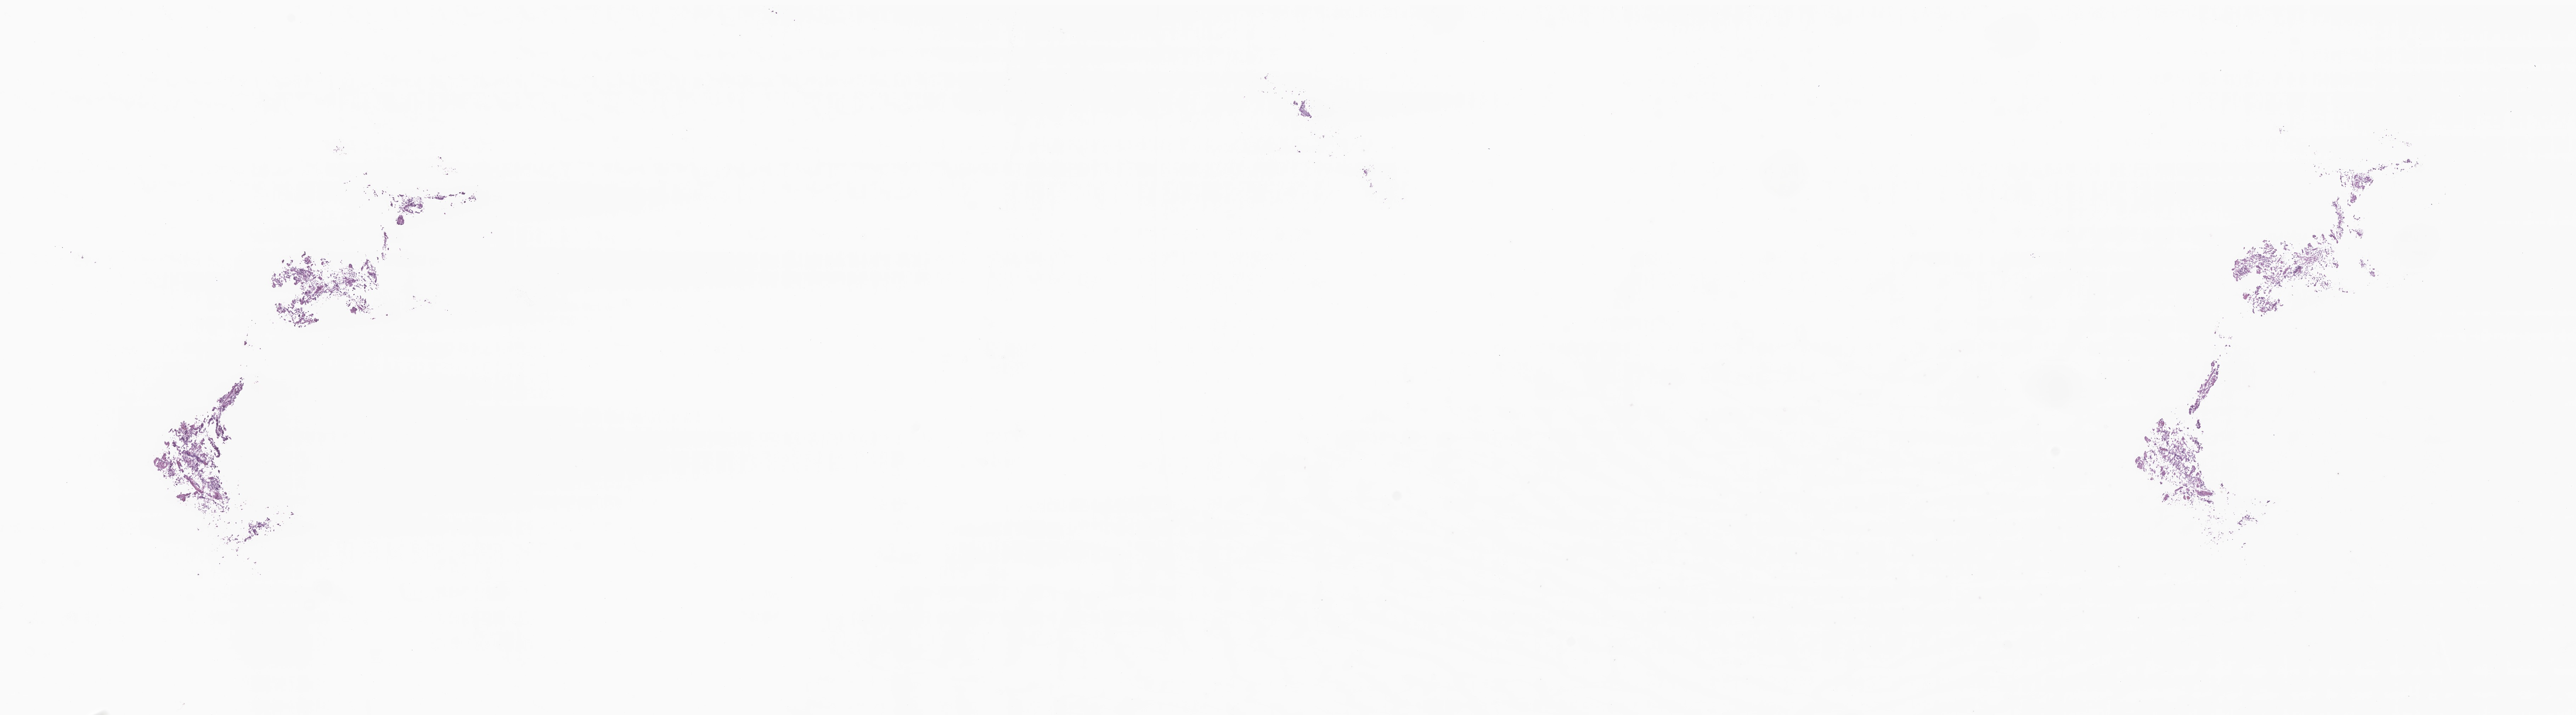
Haematoxylin and eosin whole-slide image of tumor tissue from the brain — shown as a low-resolution overview of the whole scanned area (about 30.7 x 8.5 mm), frozen section. Patient: male, age 206 months.
- diagnosis: Medulloblastoma, NOS